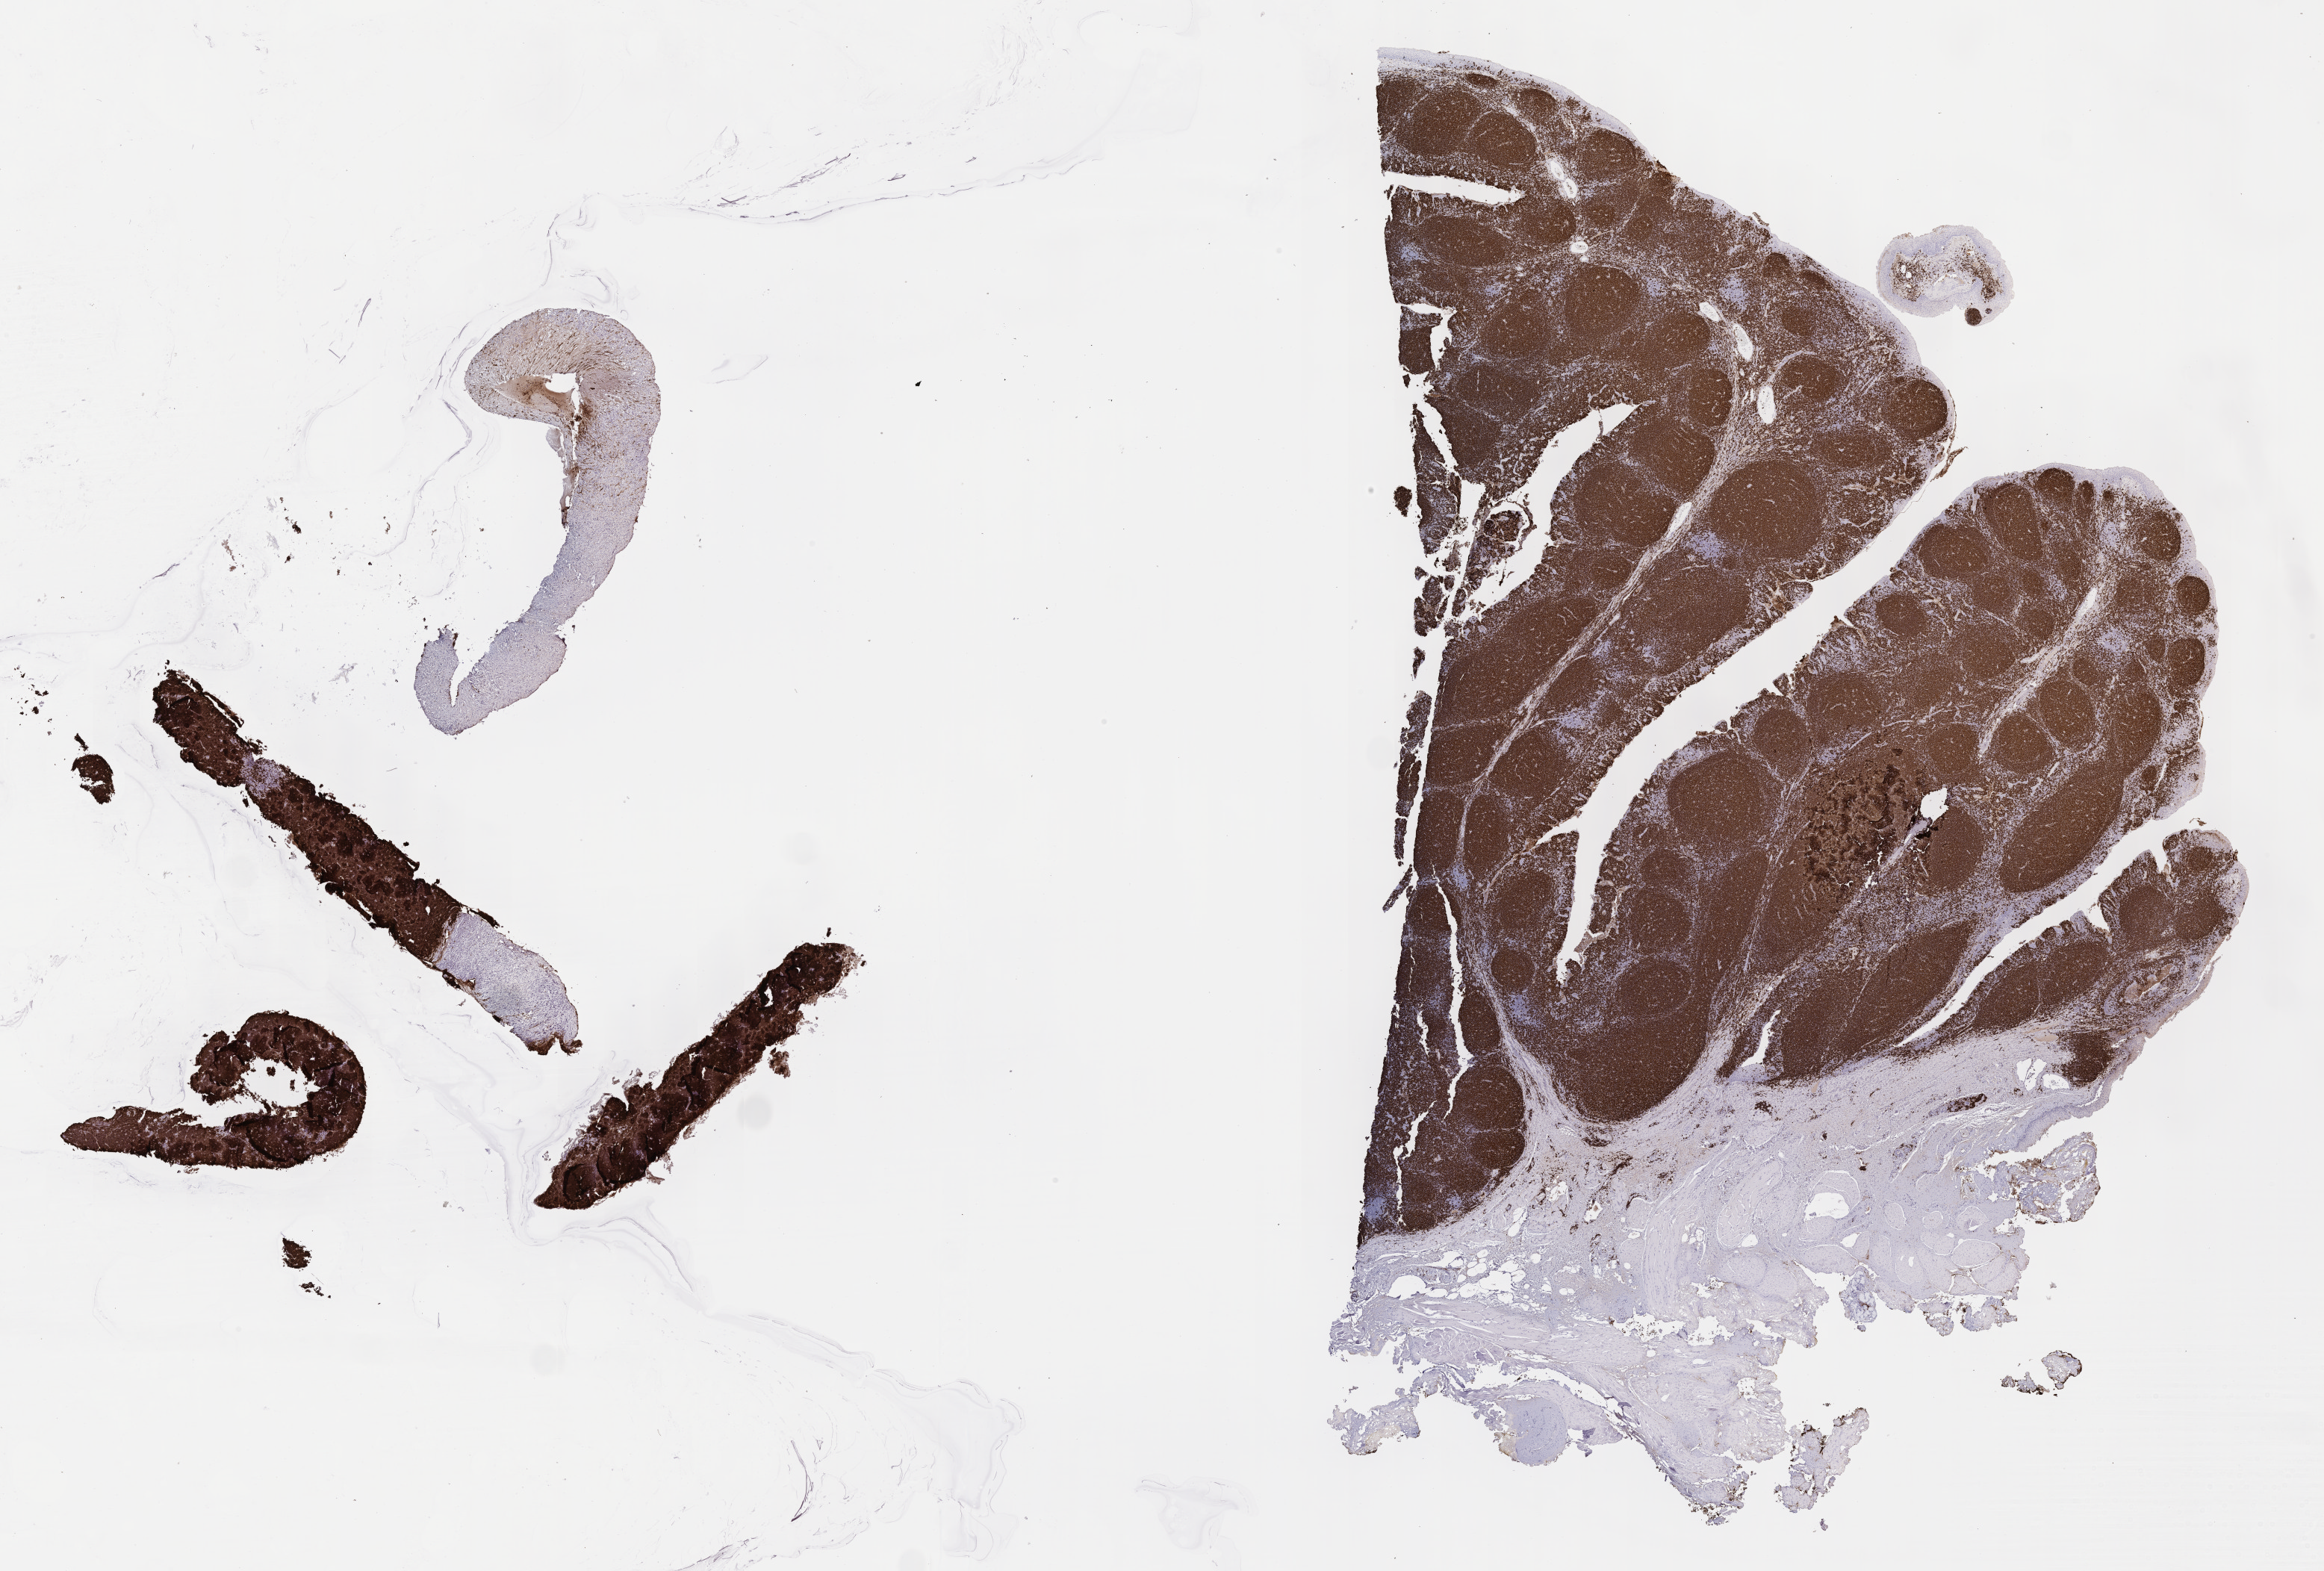
Immunohistochemistry (IHC) whole-slide image stained for CD20 — a low-resolution overview of the entire scanned area, about 25.2 x 17.0 mm. Male patient.
Specimen: tumor tissue.